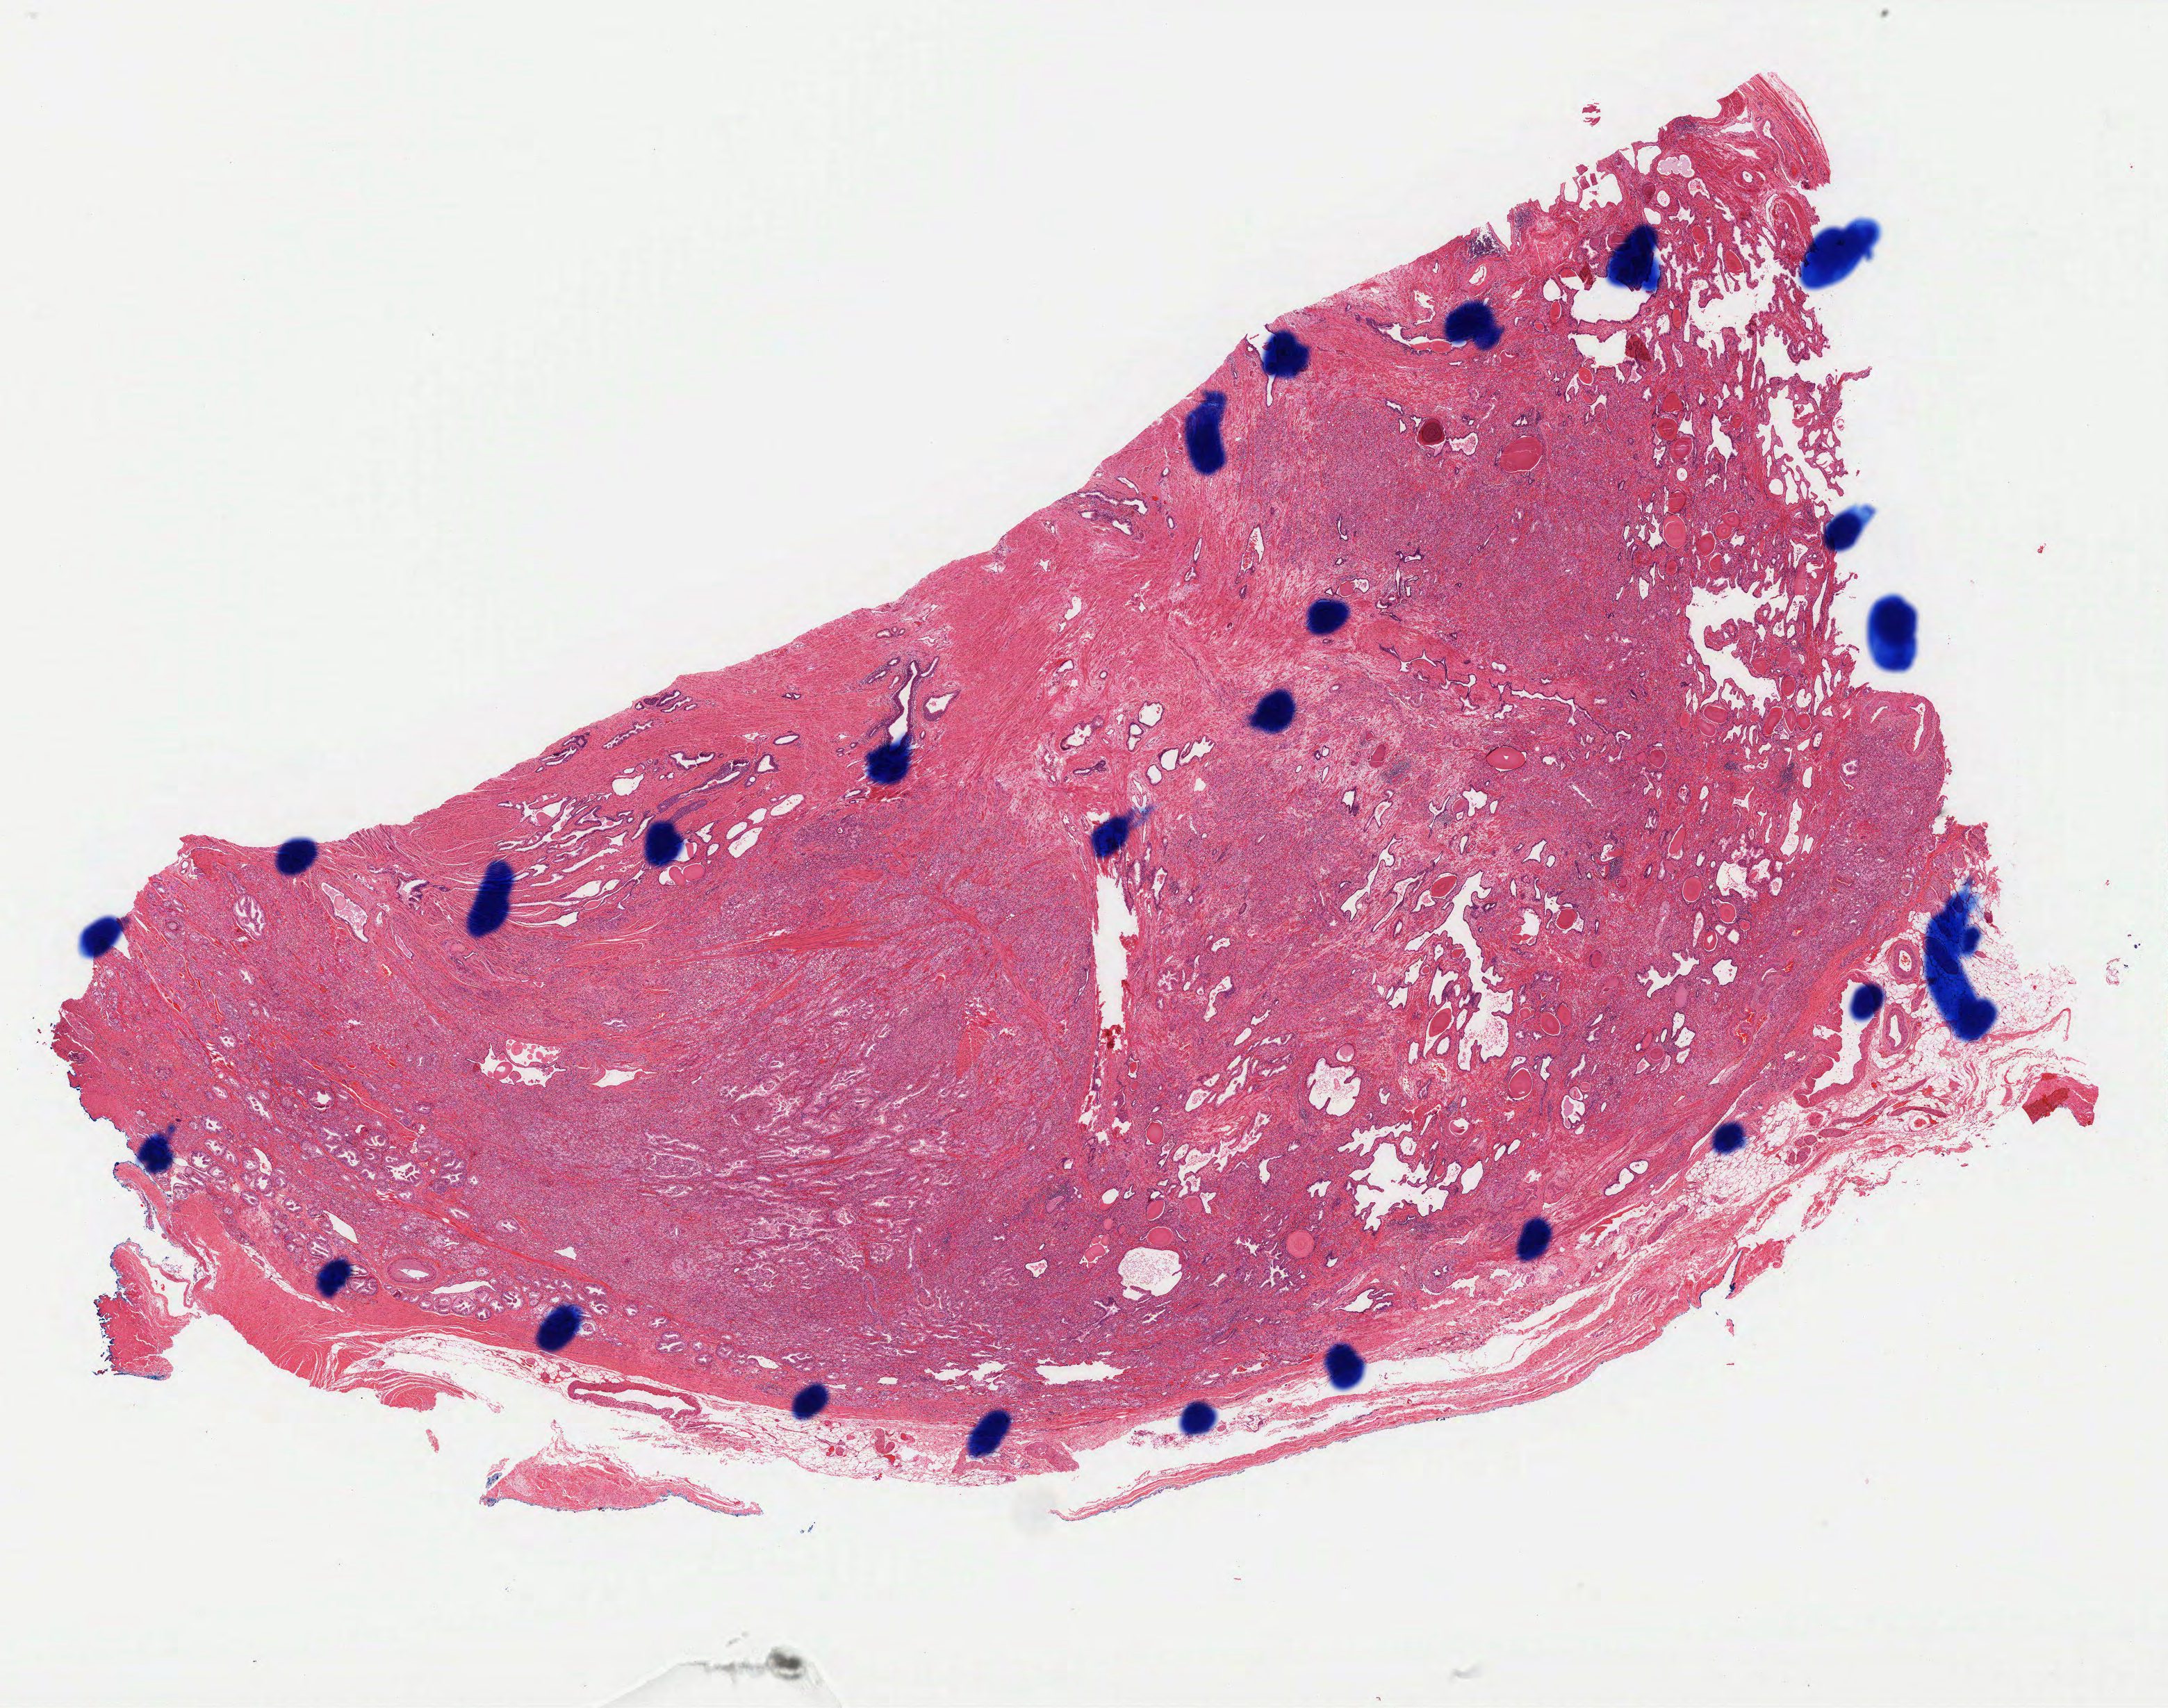
Digitized H&E-stained tissue section (whole slide) — low-resolution overview of the scanned area, about 25.0 x 19.7 mm. FFPE section. Sample: primary tumour, prostate. Patient: male, age at initial diagnosis 70 years. Gleason score: 9 (5+4).
Pathologic diagnosis: Adenocarcinoma, NOS (prostate gland).